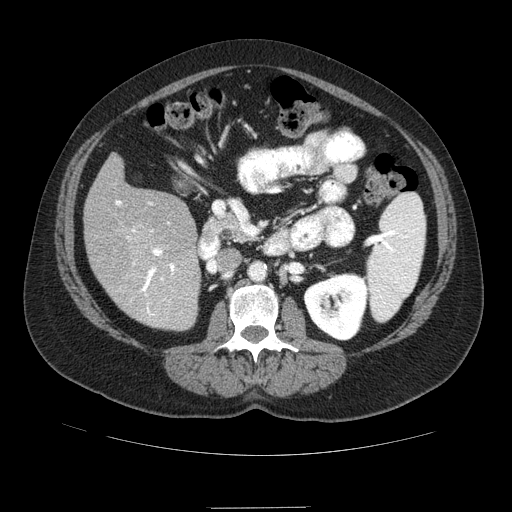
Contrast-enhanced abdominal CT (liver protocol), one axial slice; slice 33 of 89 in the series (ordered by position); 120 kVp; soft-tissue window (W 400 / L 40 HU); 512 × 512 image matrix. From the clinical record (not read from this slice): diagnosis: hepatocellular carcinoma (patient treated with transarterial chemoembolisation; whether this scan precedes or follows treatment is not stated here); TNM stage (as recorded): Stage-IIIB; Child-Pugh class: A.
Outlined on this slice (semi-automatic segmentation, software-assisted and operator-edited):
- liver parenchyma outside the tumour (the mass and vessels are separate outlines, so this box may not span the whole liver): bounding box (x1, y1, x2, y2) in pixels: (84, 154, 200, 330)
- liver vessels: (116, 201, 175, 316)